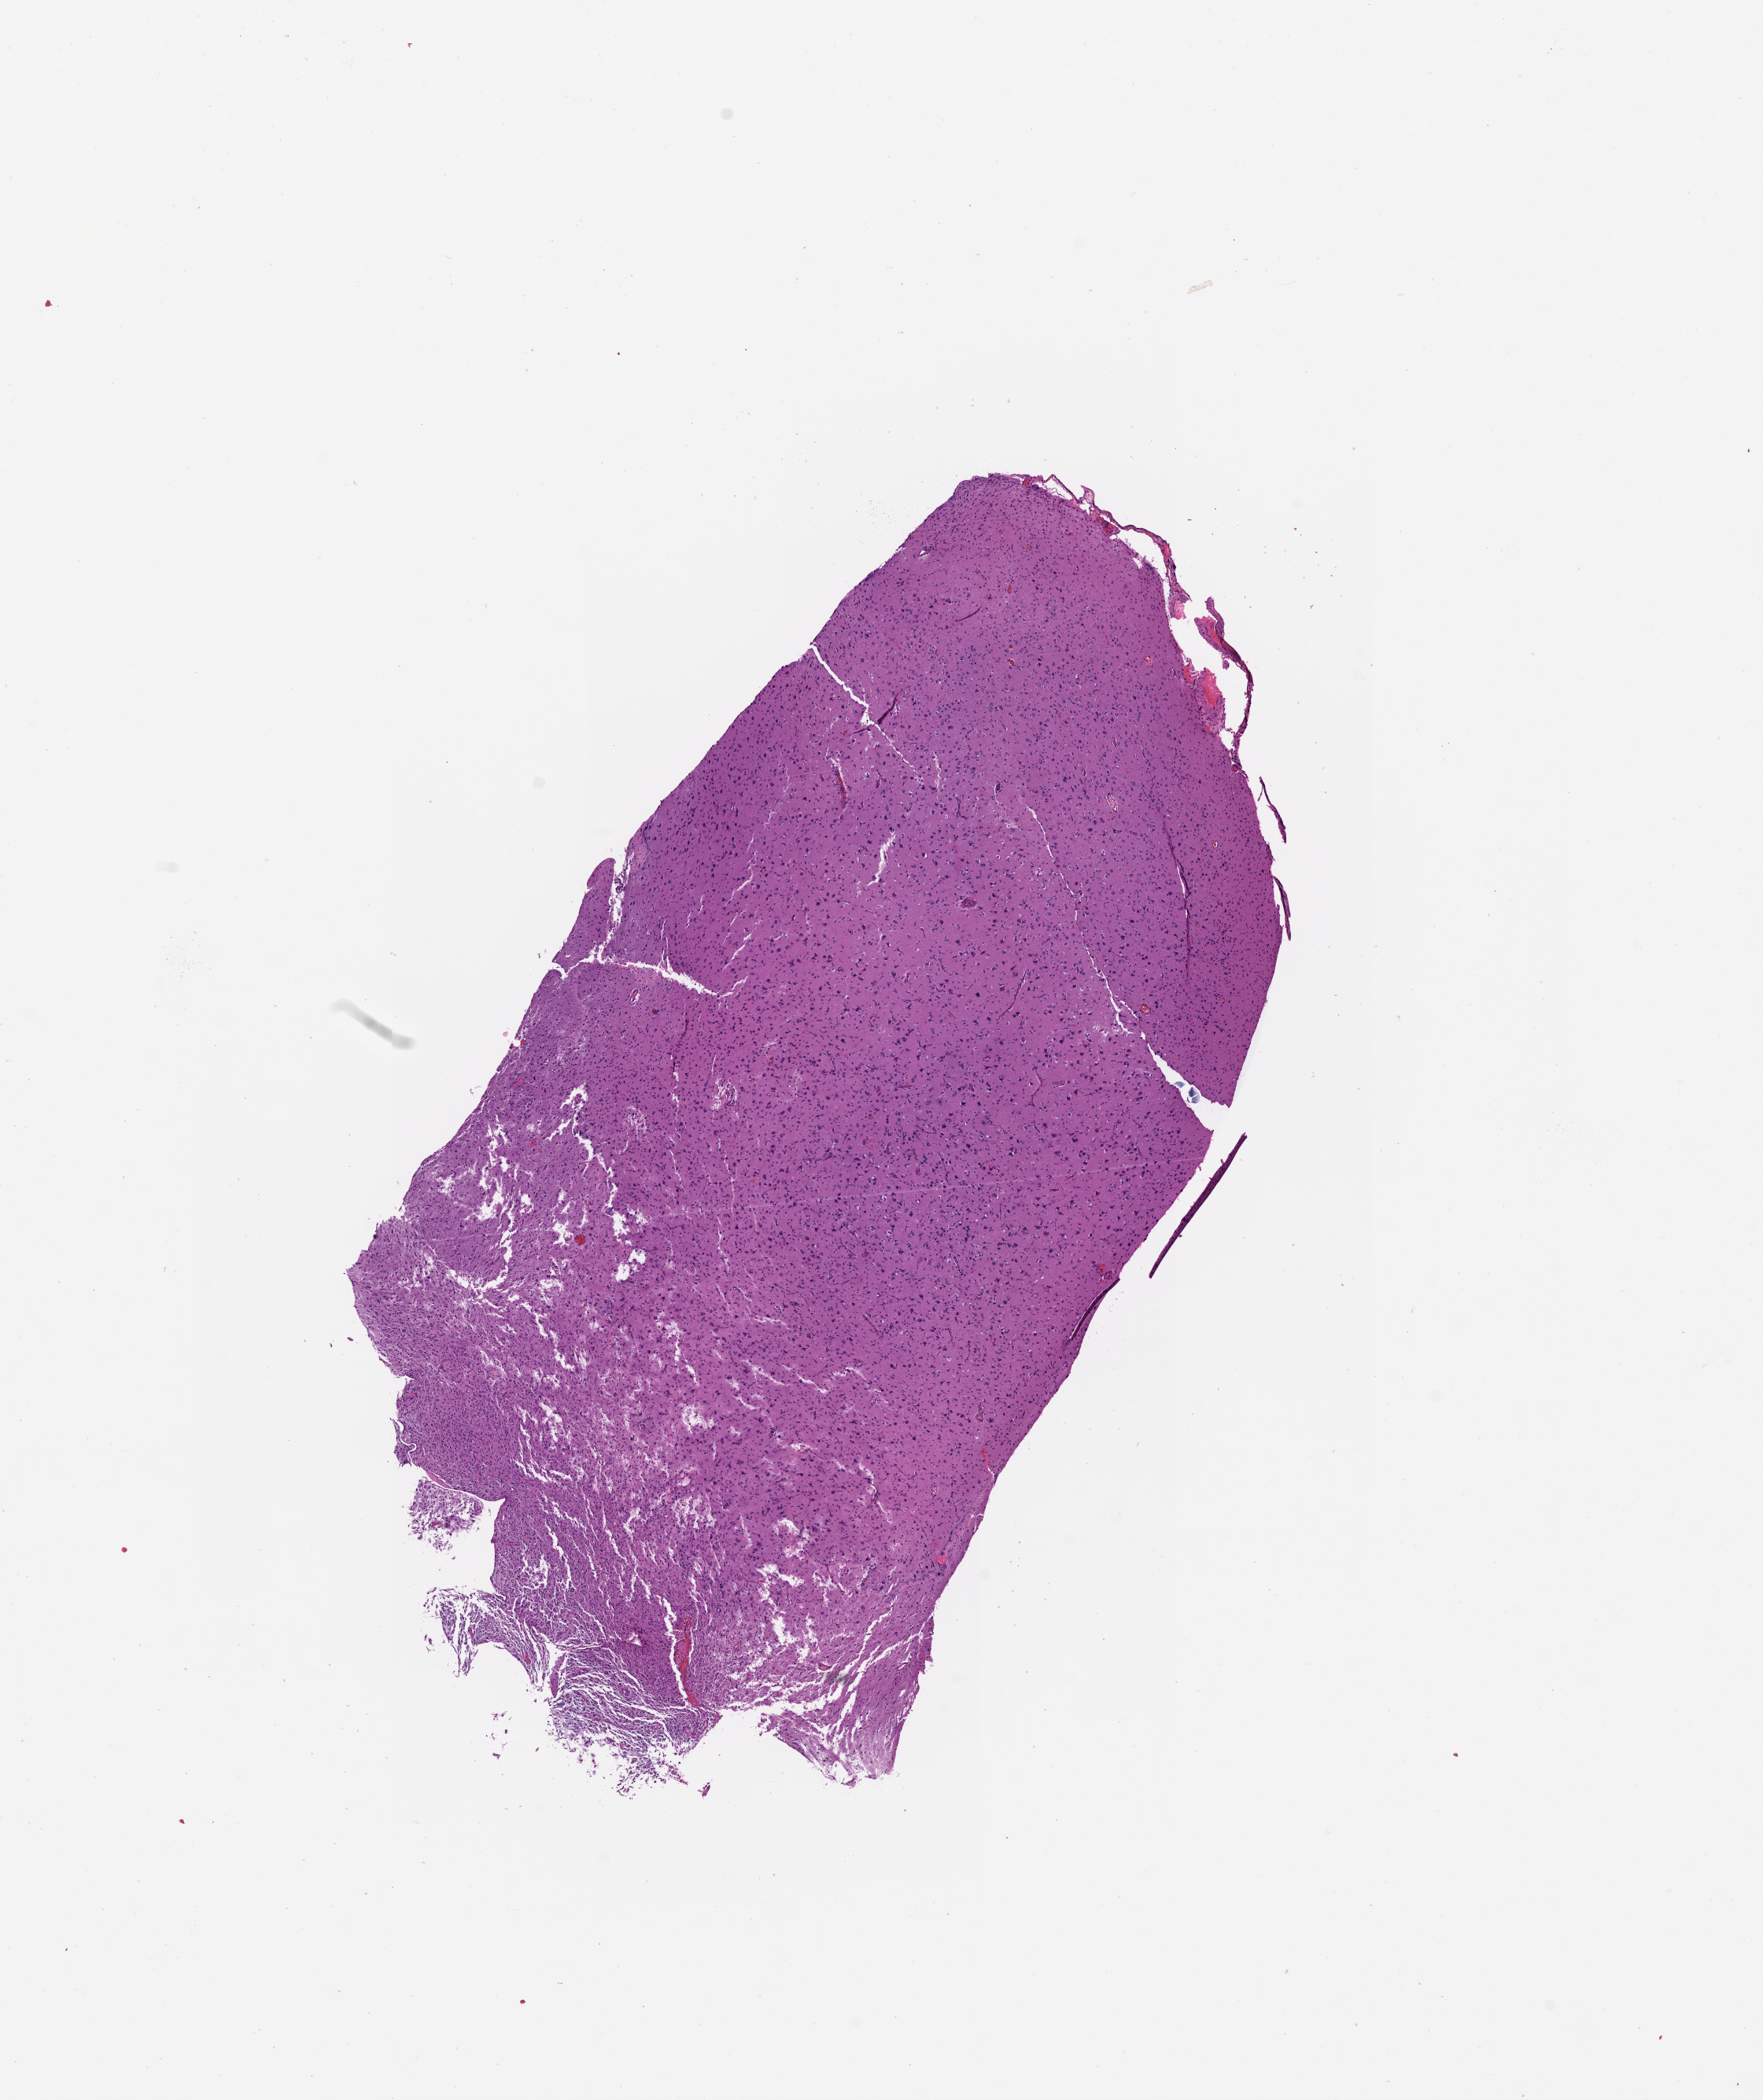
H&E whole-slide image, low-resolution overview of the scanned area, about 9.0 x 10.7 mm (acquisition: 20x scan). Tumour tissue sample, sampled site: brain. Patient: male, age 51 years. Composition of this section per pathologist review: tumour nuclei 60%, necrosis 5%.
• primary tumour site (as recorded): temporal lobe
• histologic diagnosis: Glioblastoma